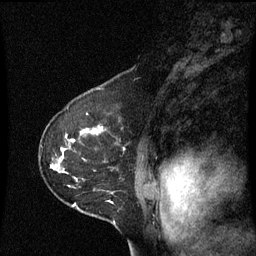
Breast MRI (dynamic contrast-enhanced), one sagittal slice; slice 45 of 60 in the series (ordered by position); dynamic contrast-enhanced series, image 2 of 3 at this slice position (ordered by acquisition); 1.5 T; TE 4.2 ms, TR 8.9 ms; 256 × 256 image matrix. Female patient, age 53 years. From the clinical record (not read from this slice): setting: breast cancer imaged before/during neoadjuvant chemotherapy; receptor status: HR-positive, HER2-negative.
Annotated regions visible in this slice (semi-automatic segmentation, software-assisted and operator-edited):
- analysis volume of interest (the breast-tissue region the enhancement analysis was run in; not a lesion): bounding box <42,104,145,221> (left, top, right, bottom; pixels)
- tumour enhancement mask (voxels above the 70 % enhancement threshold inside the analysis volume of interest): <82,128,103,135>